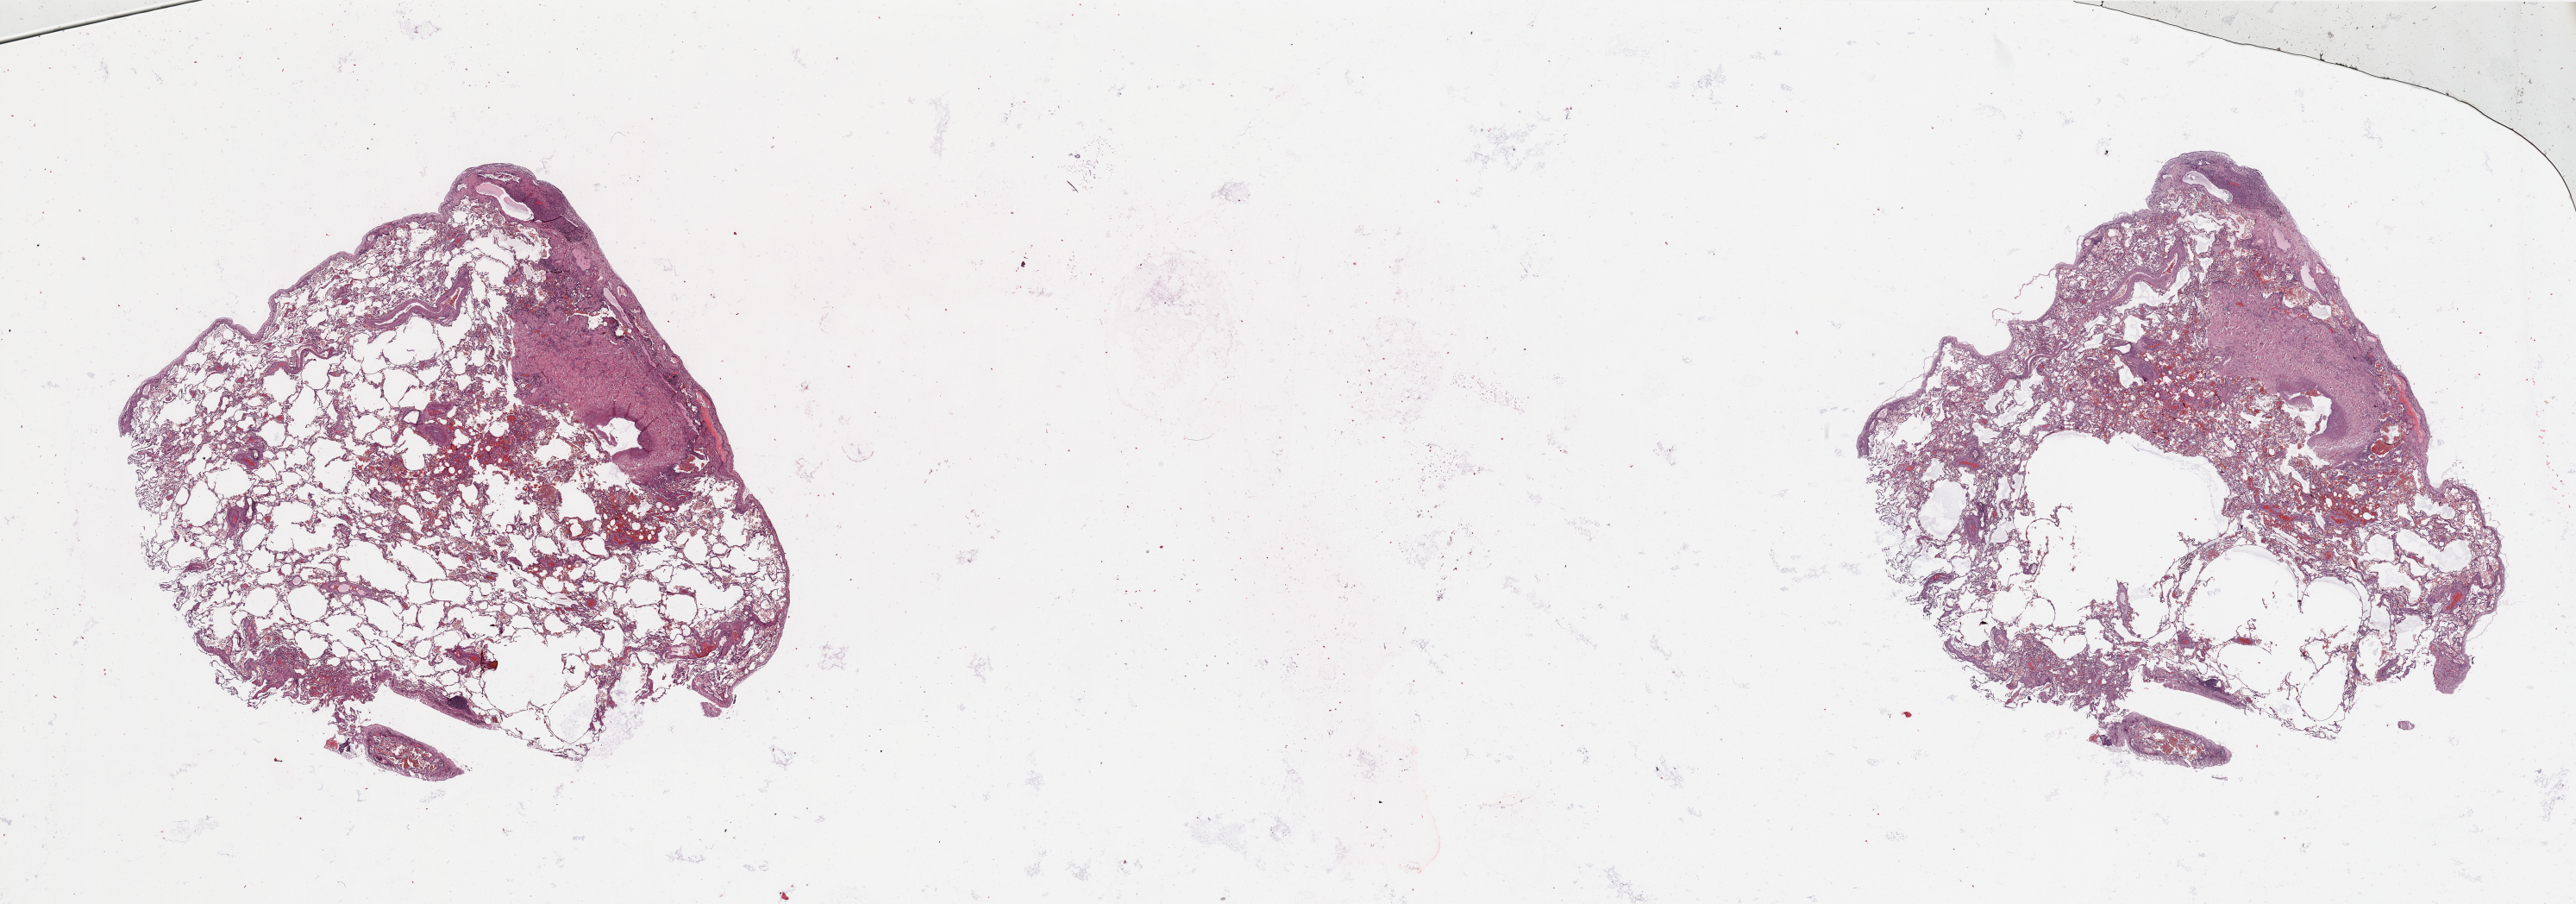
H&E whole-slide image, low-resolution overview of the scanned area, about 47.3 x 16.6 mm, normal (non-tumour) tissue sample, sampled site: lung. Male, 72 y/o.
This section: normal (non-tumour) tissue from the same patient. Patient diagnosis: Adenocarcinoma, NOS.